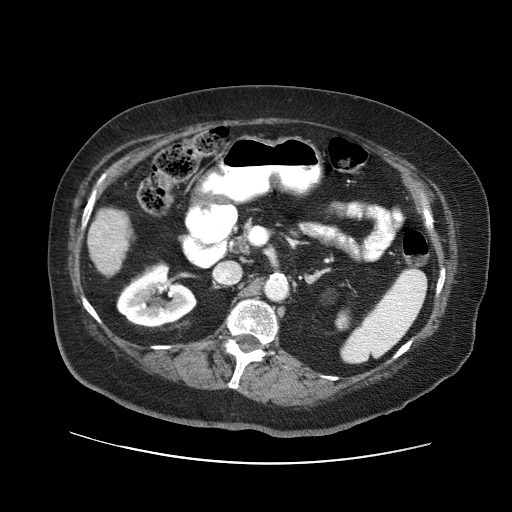
Contrast-enhanced abdominal CT (liver protocol), one axial slice; slice 13 of 71 in the series (ordered by position); reconstruction kernel STANDARD; soft-tissue window (W 400 / L 40 HU); 512 × 512 image matrix, field of view 400 × 400 mm. Case-level facts recorded for this patient, not image findings: diagnosis: hepatocellular carcinoma (patient treated with transarterial chemoembolisation; whether this scan precedes or follows treatment is not stated here); TNM stage (as recorded): Stage-II; Child-Pugh class: A; tumour differentiation: poorly differentiated; tumour size: 5 cm.
Structures marked on this image (semi-automatically segmented with operator editing):
- liver parenchyma outside the tumour (the mass and vessels are separate outlines, so this box may not span the whole liver): bounding box (x1, y1, x2, y2) in pixels: (88, 208, 132, 276)